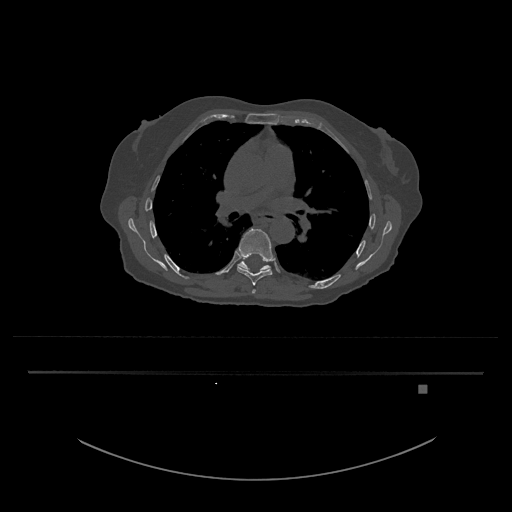
CT including the spine, one axial slice; position 794 of 797 along the scan axis; 120 kVp; bone window (W 1800 / L 400 HU); 0.5 mm slice thickness; 512 × 512 image matrix, field of view 500 × 500 mm. Patient: female, 57 years. From the clinical record (not read from this slice): primary cancer: cervical.
Structures marked on this image (semi-automatically segmented with operator editing):
- T8 vertebra: bounding box [x1, y1, x2, y2] px = [236, 228, 275, 286]
- T9 vertebra: [238, 257, 271, 272]